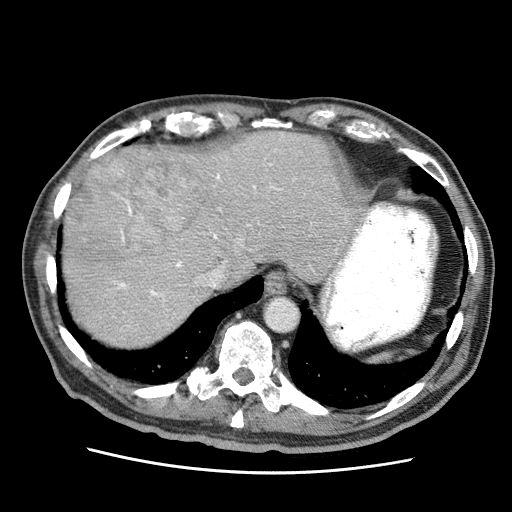
Contrast-enhanced abdominal CT (liver protocol), one axial slice. Position 53 of 75 along the scan axis. 120 kVp. Soft-tissue window (W 400 / L 40 HU). 2.5 mm slice thickness. 512 × 512 image matrix. Case-level facts recorded for this patient, not image findings: diagnosis: hepatocellular carcinoma (patient treated with transarterial chemoembolisation; whether this scan precedes or follows treatment is not stated here); TNM stage (as recorded): Stage-IIIA; Child-Pugh class: A; tumour differentiation: well differentiated; tumour nodularity: multinodular.
Outlined on this slice (semi-automatic segmentation, software-assisted and operator-edited):
- abdominal aorta: bounding box [x1, y1, x2, y2] px = [267, 298, 297, 330]
- liver parenchyma outside the tumour (the mass and vessels are separate outlines, so this box may not span the whole liver): [62, 132, 360, 346]
- mass: [66, 145, 207, 303]
- liver vessels: [114, 135, 284, 313]